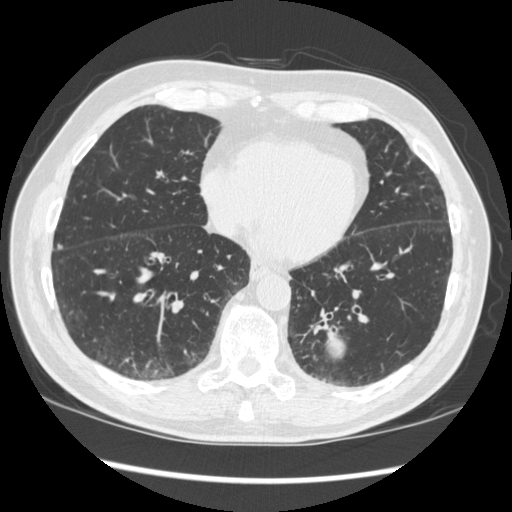
Low-dose screening chest CT, one axial slice; slice 114 of 348 in the series (ordered by position); reconstruction kernel STANDARD; lung window (W 1500 / L -600 HU); 1.25 mm slice thickness; 512 × 512 image matrix.
Annotated regions visible in this slice (outlined manually by an expert reader):
- lesion 1 (tumor, lower lobe of left lung): bounding box [x1, y1, x2, y2] px = [326, 327, 345, 360]